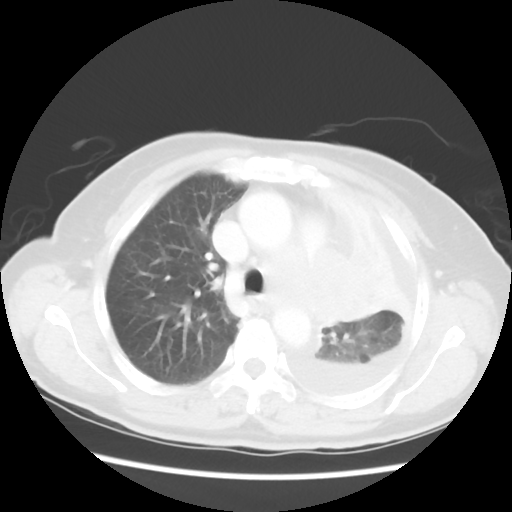
Chest CT, one axial slice; slice 37 of 52 in the series (ordered by position); 120 kVp; lung window (W 1500 / L -600 HU); 512 × 512 image matrix. Female patient, age 72 years. Case-level facts recorded for this patient, not image findings: clinical TNM (as recorded): T4 N3 M1b; histopathological grade: G3.
Structures marked on this image (bounding box drawn by a radiologist):
- lung tumour (recorded histology: large cell carcinoma): box from (x=298, y=246) to (x=371, y=338) px